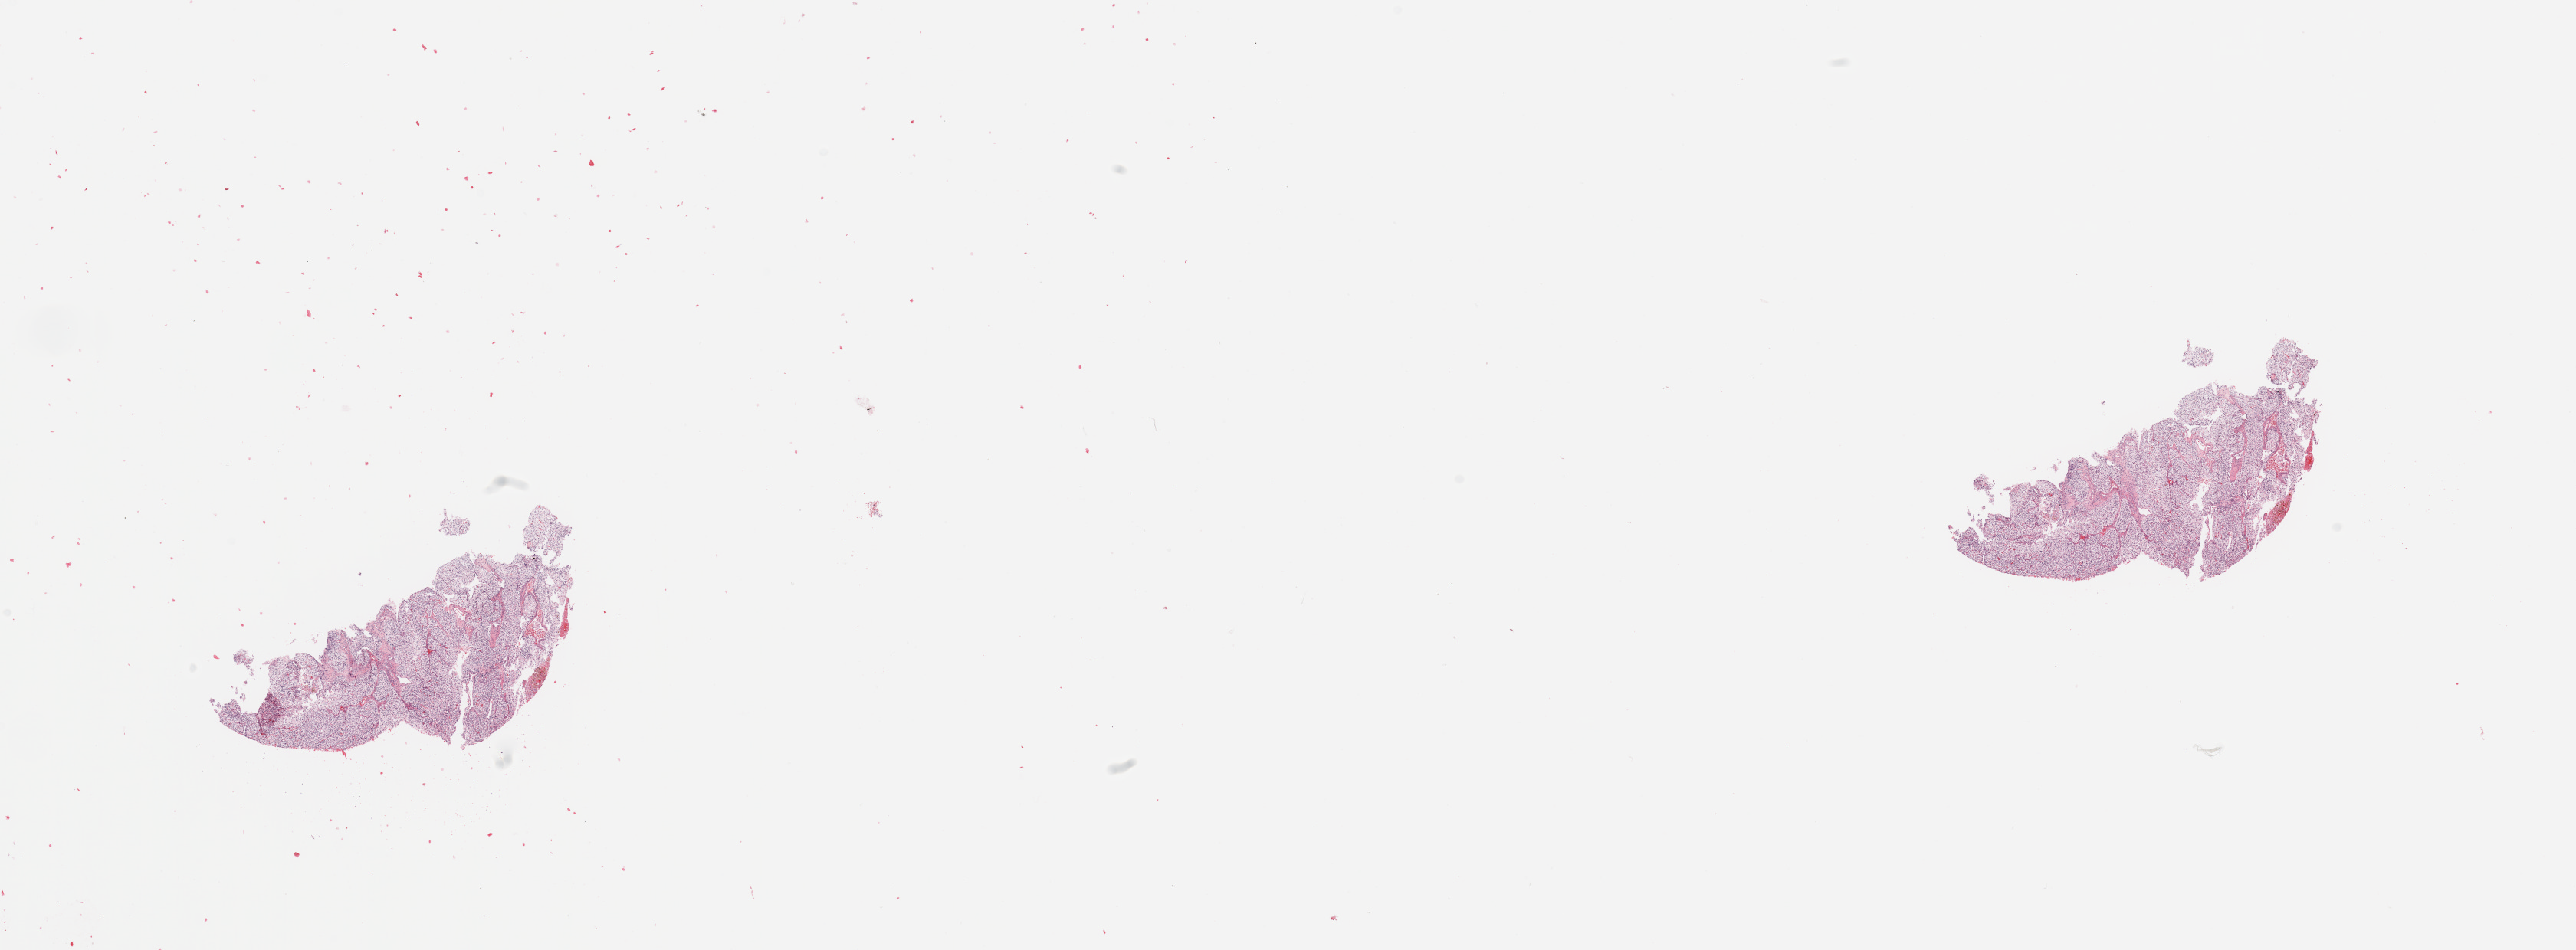
Whole-slide histology image, H&E, shown as a low-resolution overview of the whole scanned area (about 26.6 x 9.8 mm, from a 20x scan), tumour tissue sample, sampled site: kidney. Male, 44 y/o. Histologic grade: G2 (moderately differentiated). Composition of this section per pathologist review: tumour nuclei 90%, necrosis 2%.
* primary tumour site (as recorded): lower pole
* AJCC pathologic stage: I
* histologic diagnosis: Renal cell carcinoma, NOS